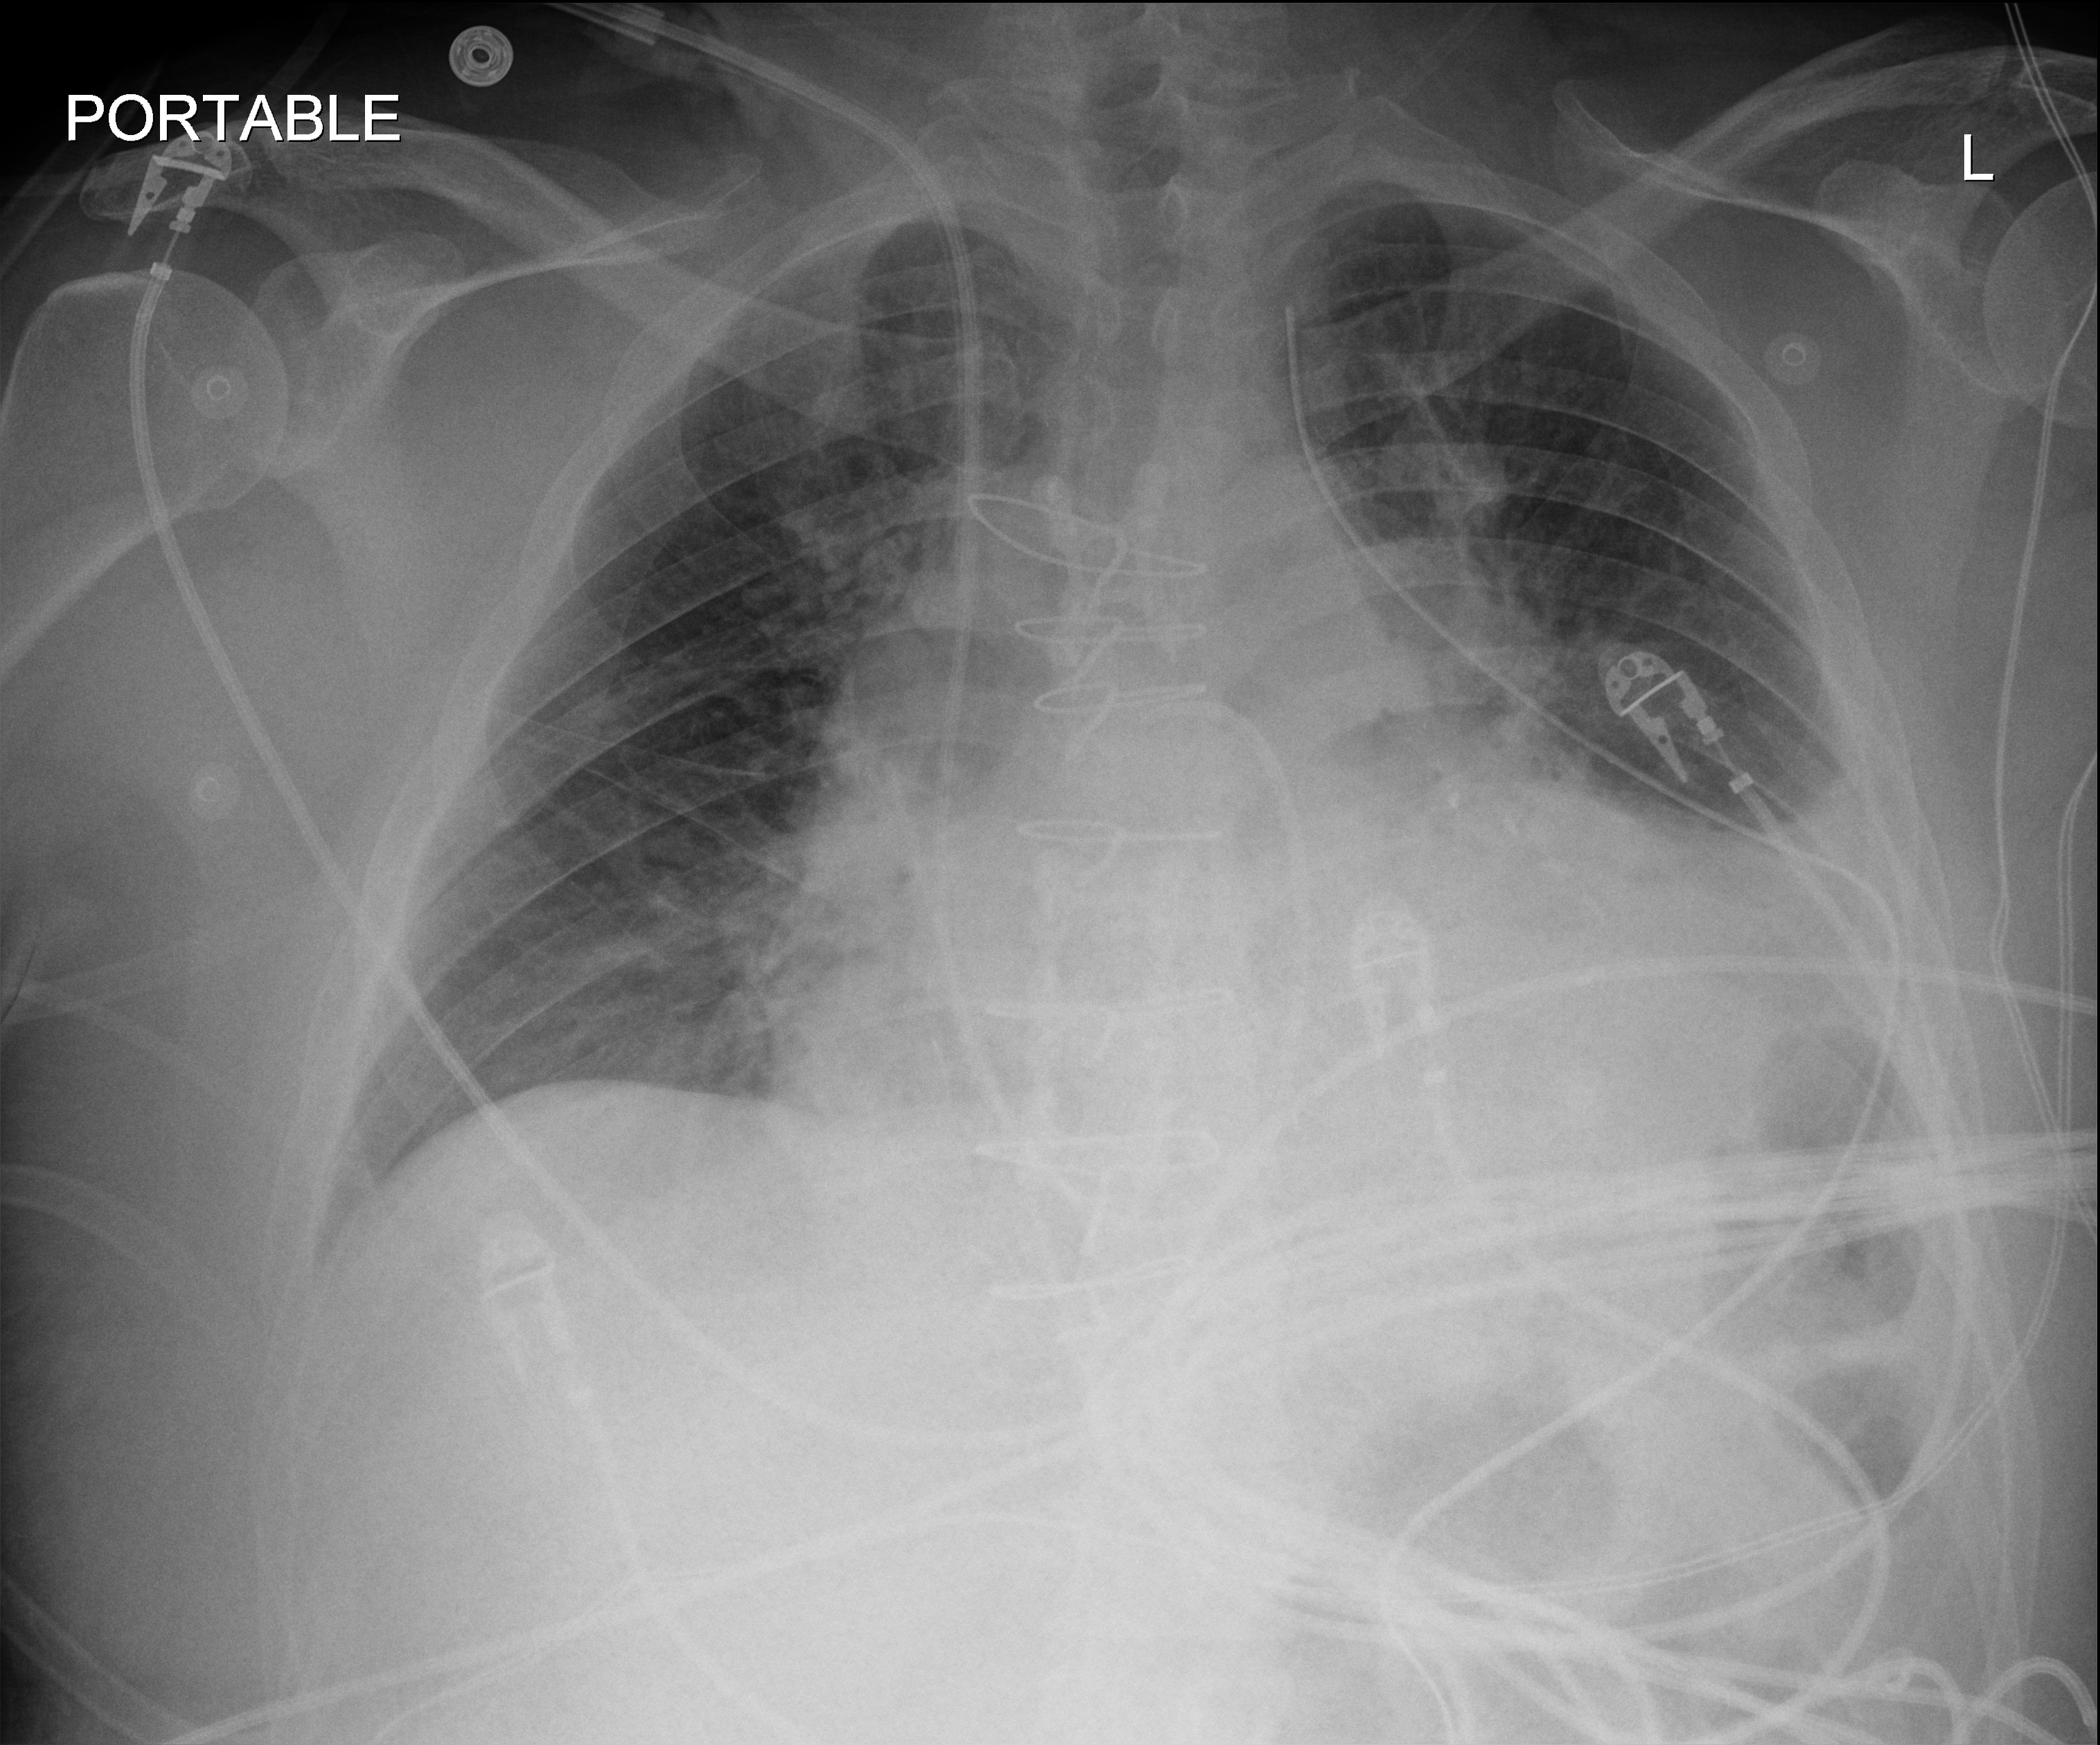
Bedside chest radiograph (digital radiography). Male patient hospitalised with COVID-19, age 18–59 years.
From the hospital-stay record, not from the radiograph (when in the stay this image was taken is not recorded):
- admitted to intensive care during this hospital stay: no